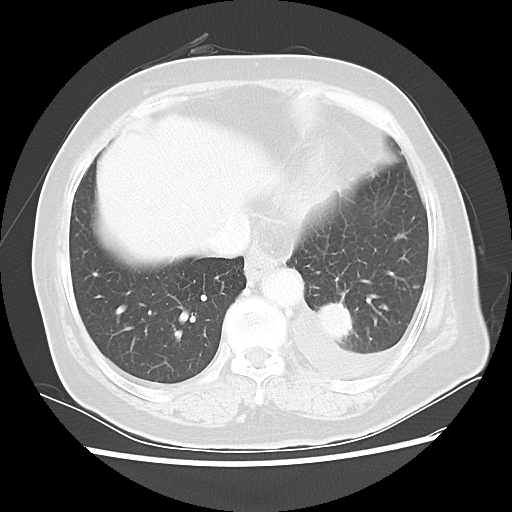
Chest CT, one axial slice; slice 8 of 40 in the series (ordered by position); reconstruction kernel LUNG; lung window (W 1500 / L -600 HU); 512 × 512 image matrix, field of view 343 × 343 mm. Female patient, age 68 years. Case-level facts recorded for this patient, not image findings: clinical TNM (as recorded): T1c N0 M1.
Annotated regions visible in this slice (rectangle marked by the reading radiologist):
- lung tumour (recorded histology: adenocarcinoma): bounding box [x1, y1, x2, y2] px = [316, 300, 356, 347]